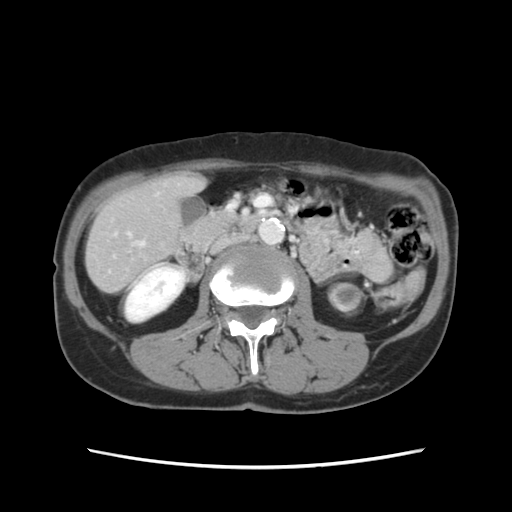
Contrast-enhanced abdominal CT, one axial slice; slice 36 of 120 in the series (ordered by position); soft-tissue window (W 400 / L 40 HU); 2.5 mm slice thickness; 512 × 512 image matrix, field of view 330 × 330 mm. Female patient, age 70 years. From the clinical record (not read from this slice): diagnosis: colorectal cancer liver metastases, imaged before liver resection; multiple liver metastases: no; largest metastasis: 2.5 cm; disease in both lobes: no.
Annotated regions visible in this slice (manually delineated by an expert):
- hepatic veins: bounding box [x1, y1, x2, y2] px = [138, 242, 143, 246]
- liver: [85, 176, 202, 292]
- planned liver remnant (the part of the liver to remain after resection): [85, 175, 202, 292]
- portal vein (with intrahepatic branches): [128, 233, 131, 237]